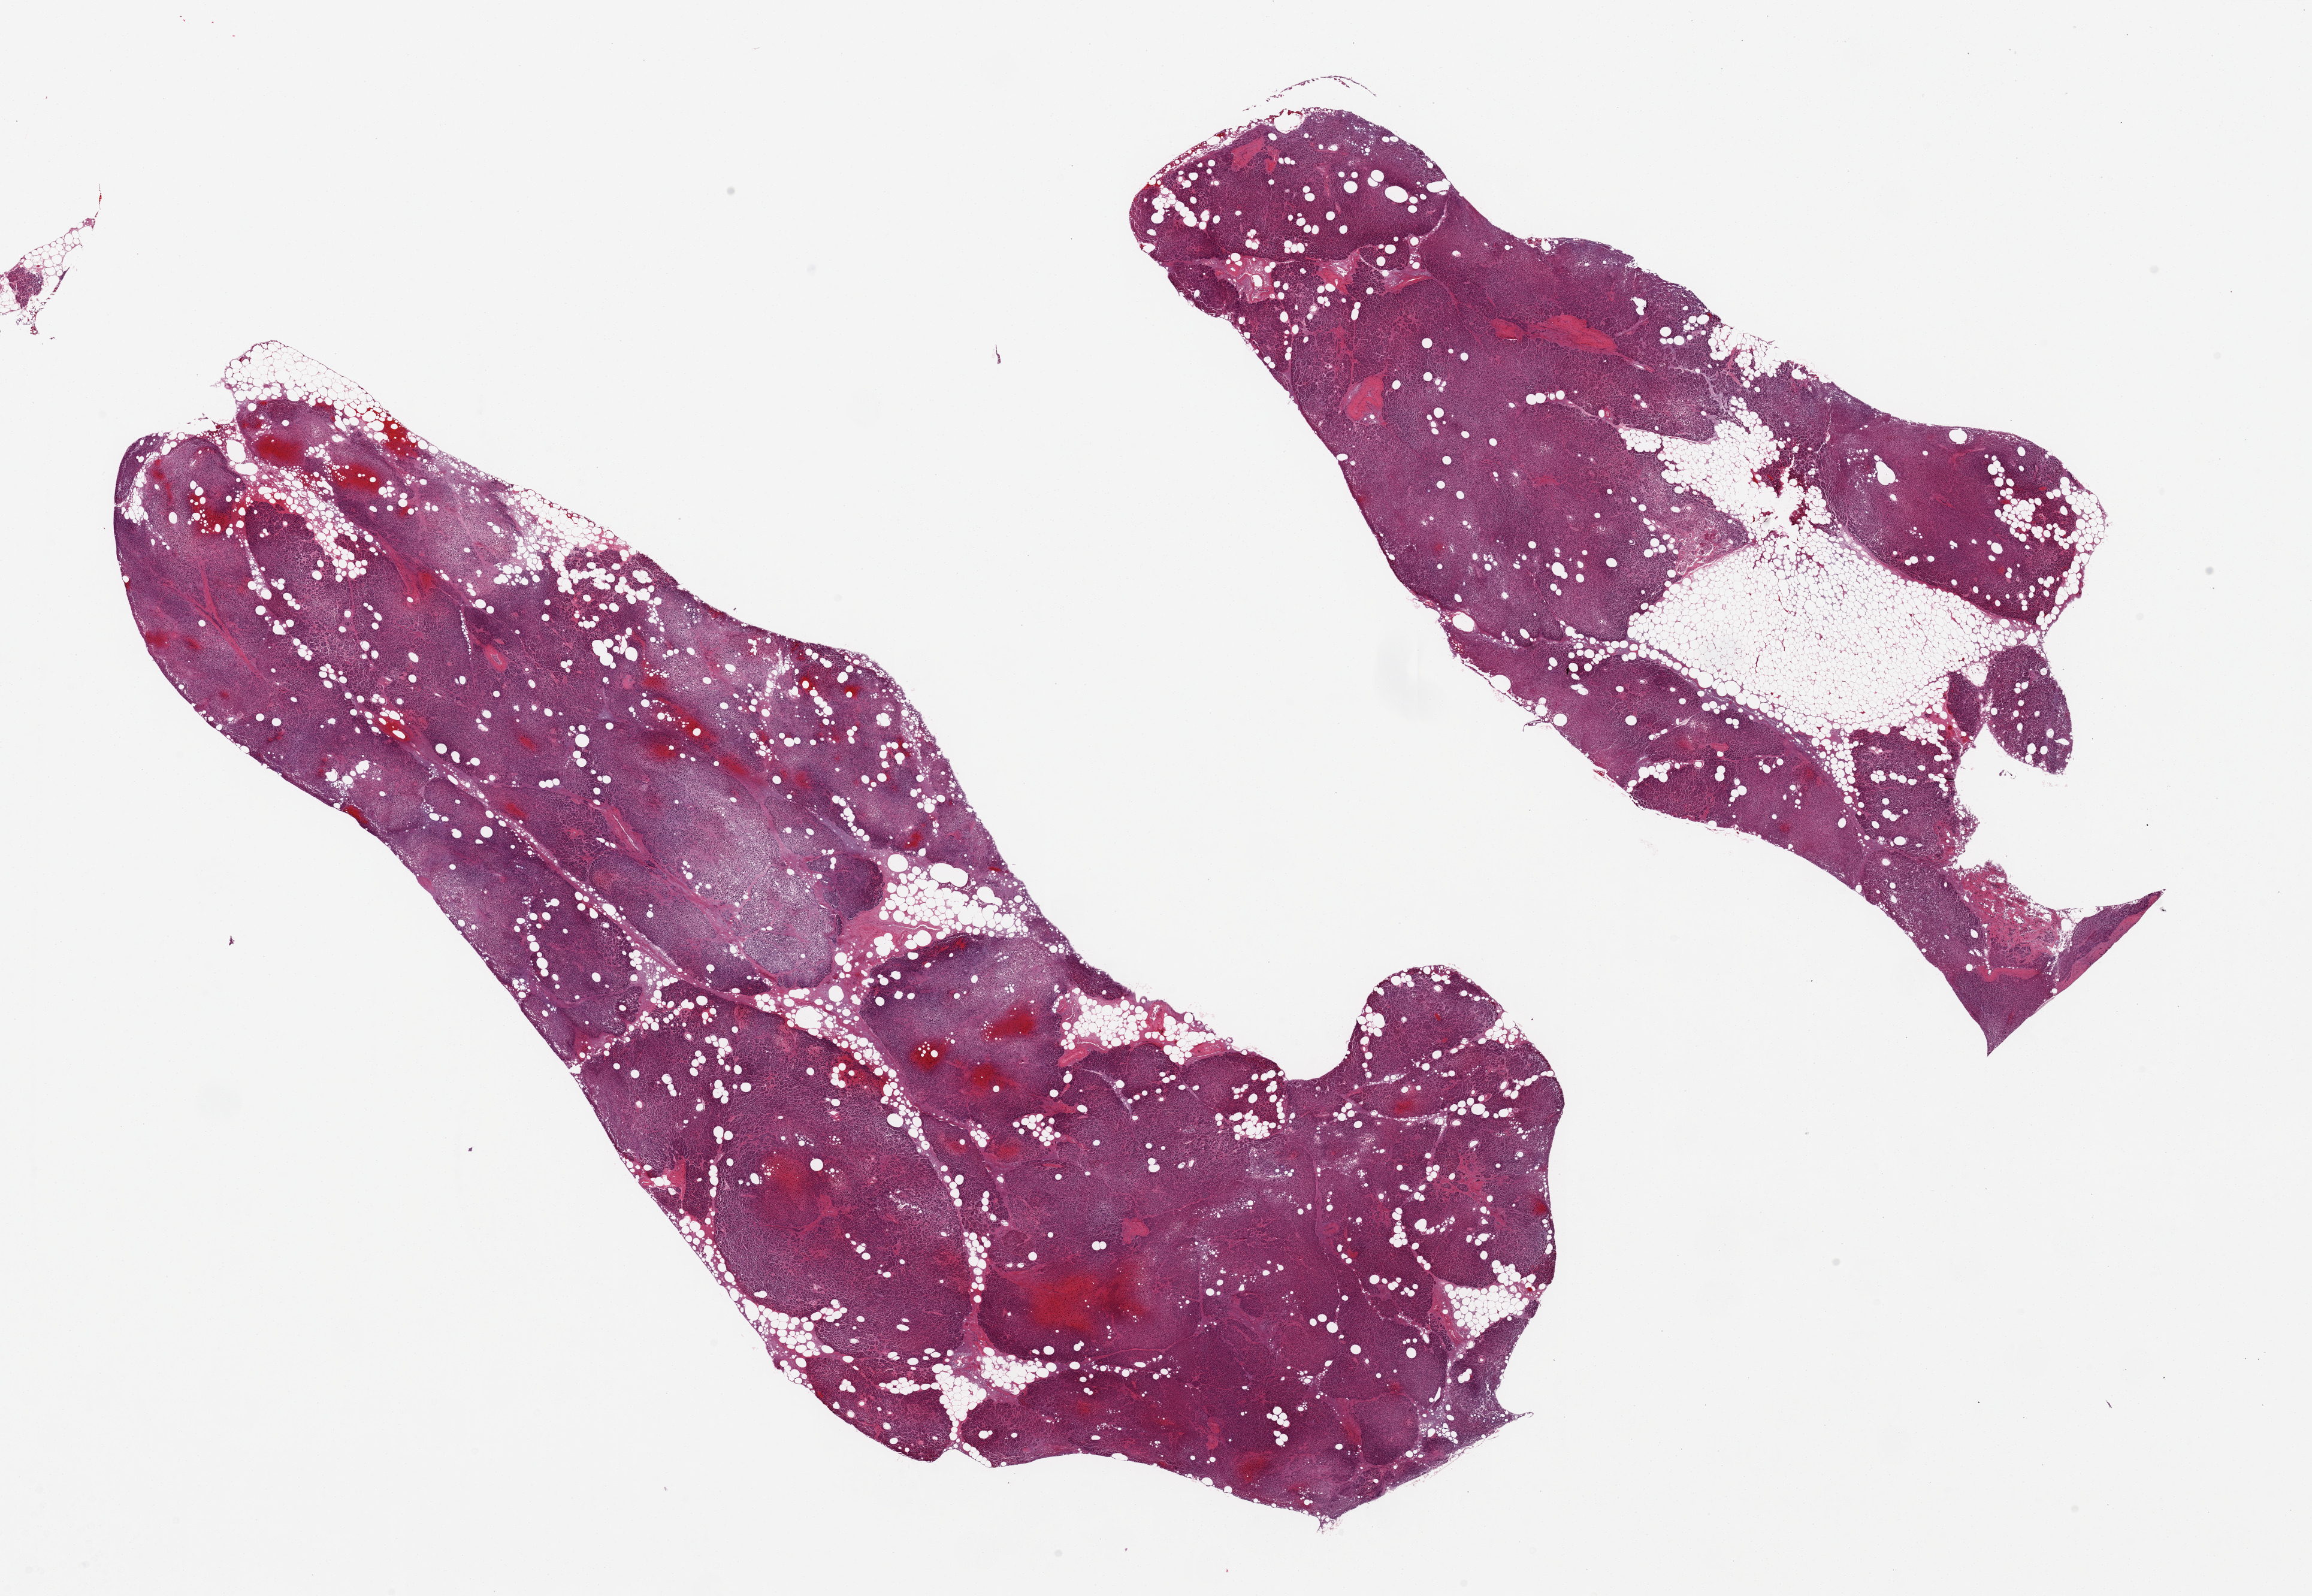
Digitized hematoxylin and eosin (H&E)-stained section, a low-resolution overview of the entire scanned area, about 30.5 x 21.1 mm (slide scanned at 20x), PAXgene-fixed, paraffin-embedded tissue, target tissue: pancreas, tissue donor sample. Donor sex: male.
Pathologist's review note for this sample: 2 pieces; severe autolysis and 30 & 50% internal fat.